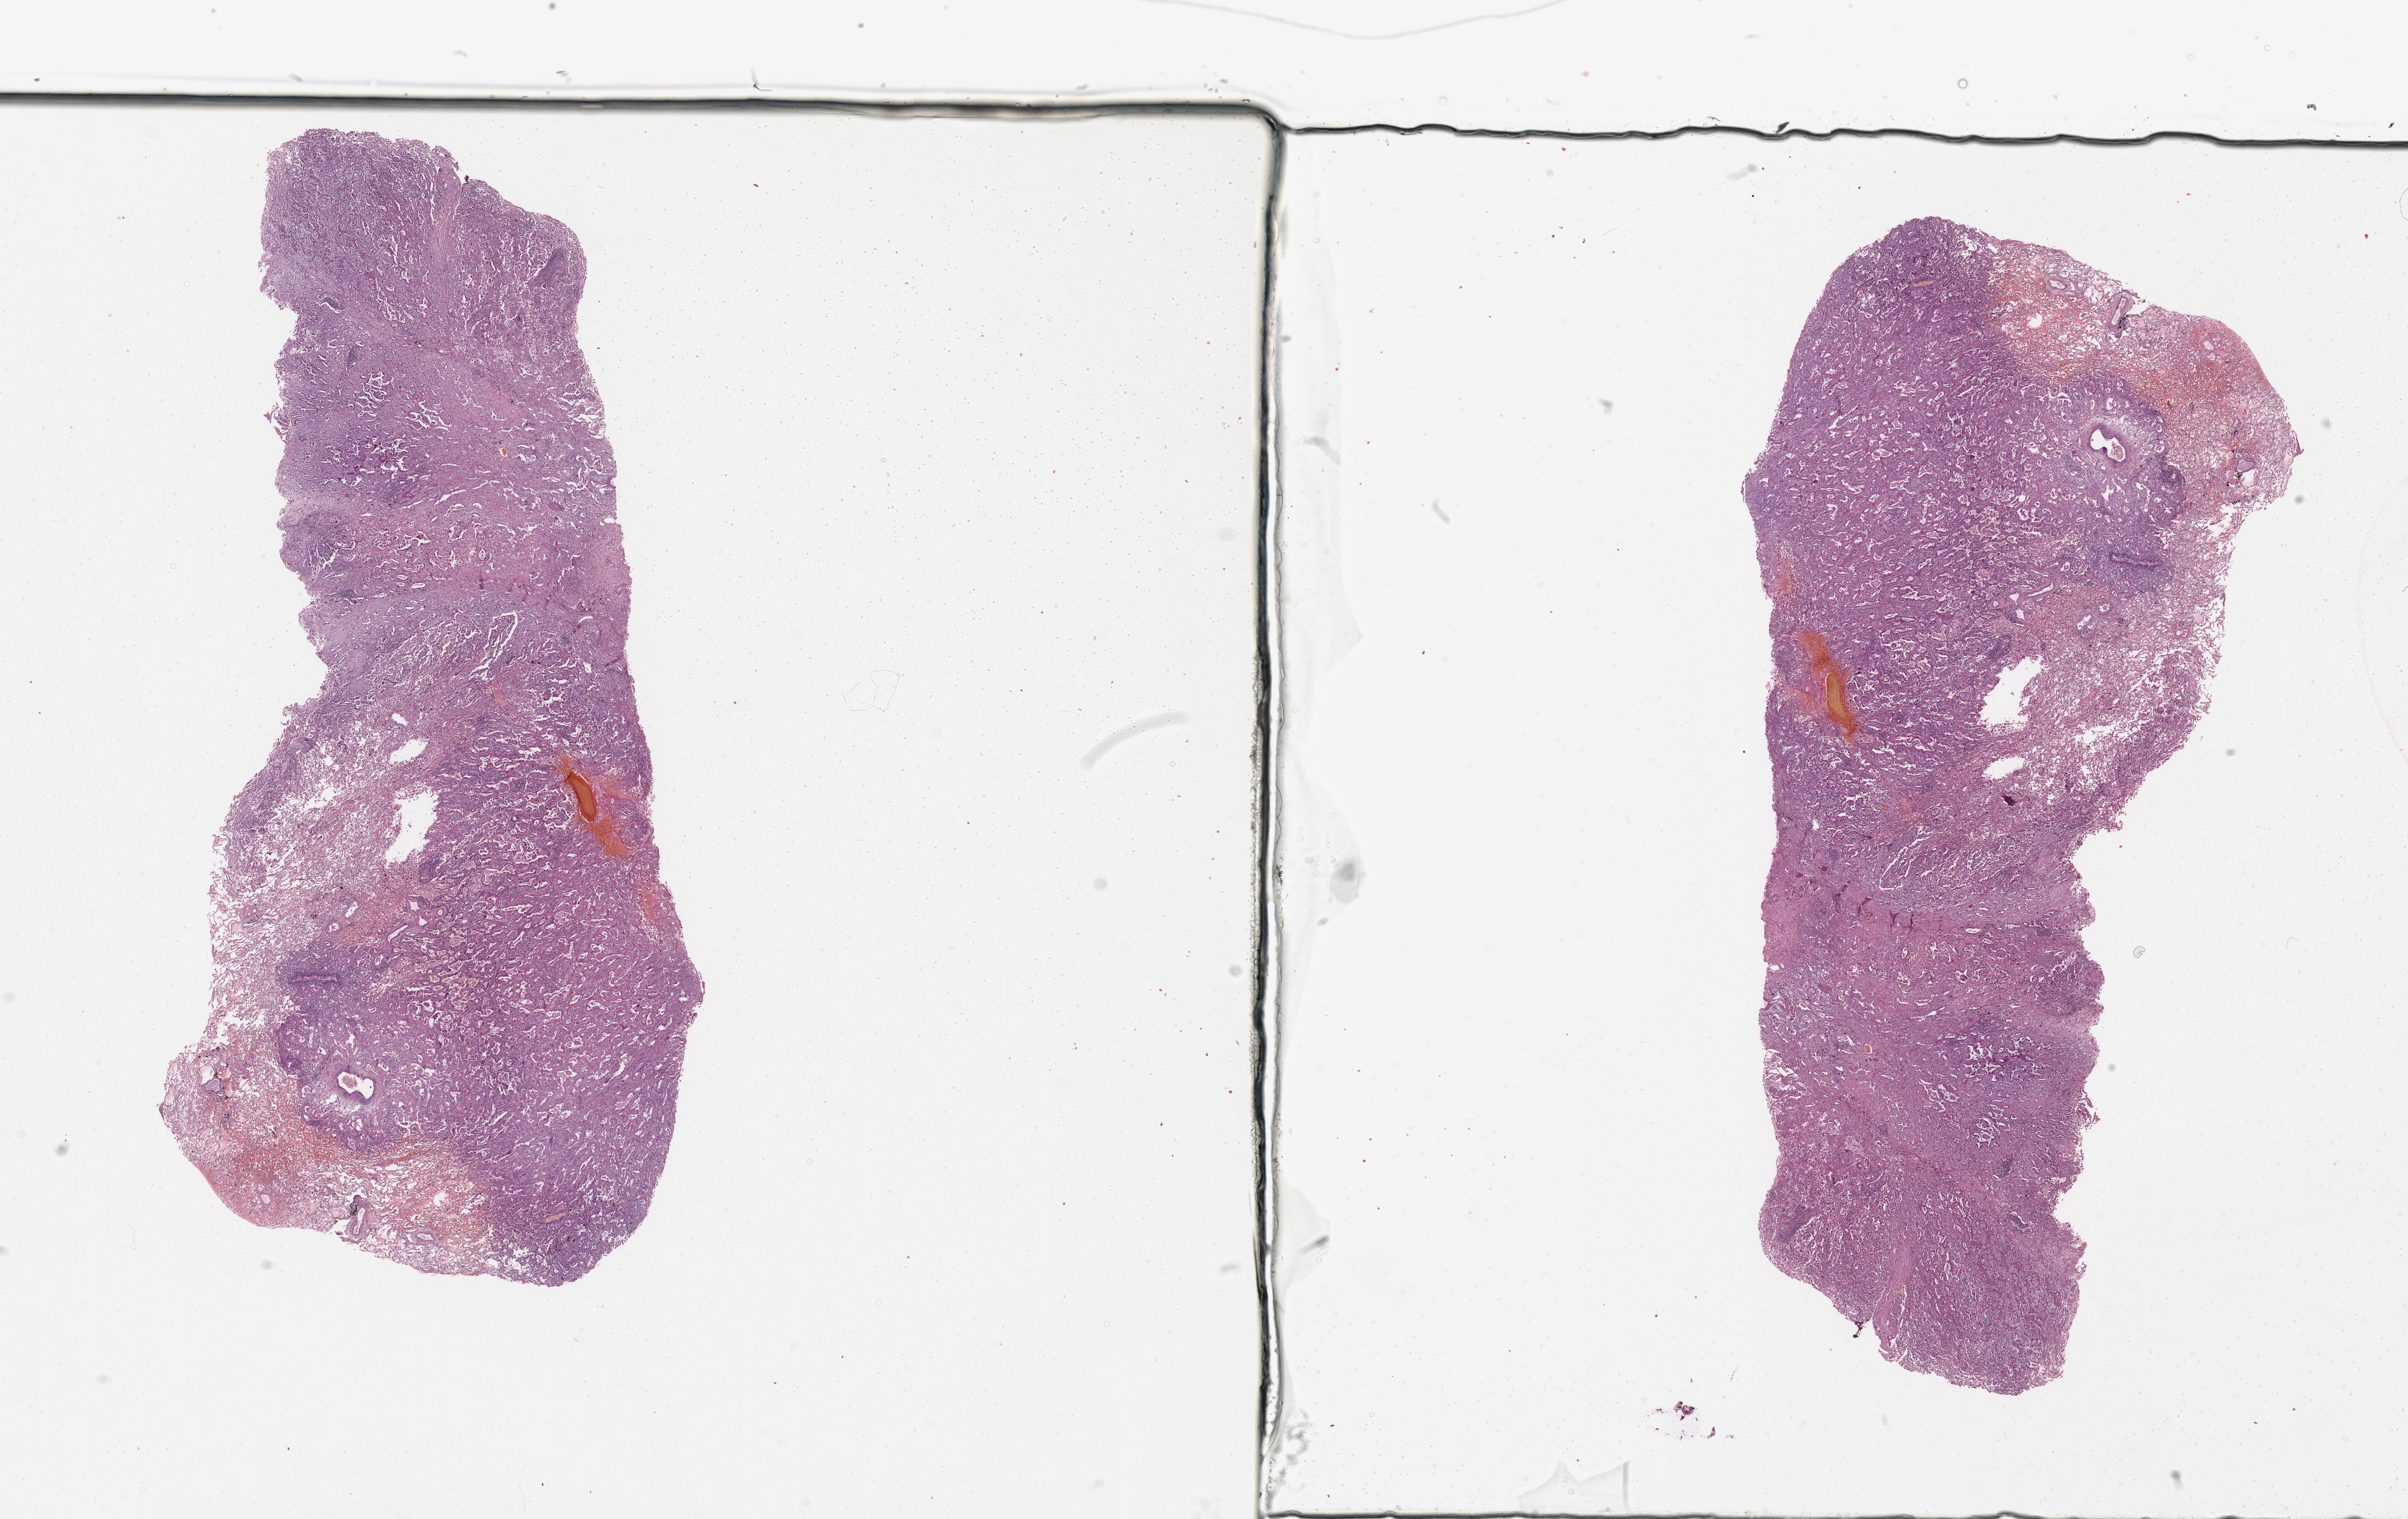
Whole-slide histology image, Hematoxylin and eosin (H&E) stained, low-resolution overview of the scanned area, about 28.5 x 18.0 mm (slide scanned at 20x), tumour tissue sample, lung. 63-year-old female patient. Histologic grade: G2 (moderately differentiated).
* histologic diagnosis: Adenocarcinoma, NOS
* AJCC pathologic stage: IB
* primary tumour site (as recorded): right upper lobe